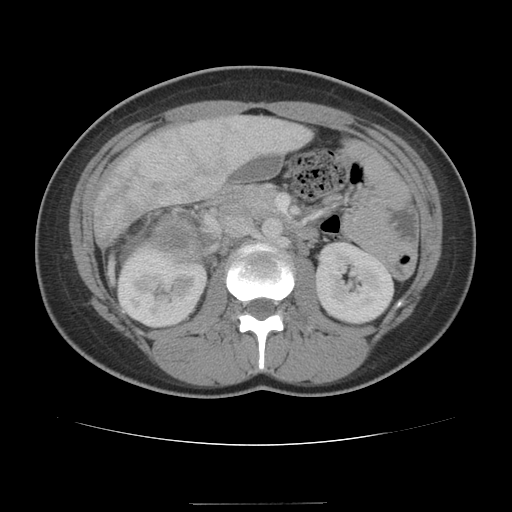
Contrast-enhanced abdominal CT, one axial slice. Position 60 of 100 along the scan axis. 120 kVp. Intravenous contrast given. Soft-tissue window (W 400 / L 40 HU). 5 mm slice thickness. 512 × 512 image matrix, field of view 360 × 360 mm. Patient: female, 21 years. From the clinical record (not read from this slice): diagnosis: adrenocortical carcinoma; tumour side: right adrenal; tumour size at pathology: 15.5 cm.
Annotated regions visible in this slice (semi-automatically segmented with operator editing):
- mass: box from (x=155, y=218) to (x=200, y=259) px